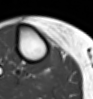
MRI of an extremity soft-tissue mass, one axial slice; slice 33 of 54 in the series (ordered by position); MR volume resampled by the dataset authors to the PET/CT grid (not the native acquisition matrix); 3.27 mm slice thickness; 93 × 99 image matrix, field of view 91 × 97 mm. Female patient. From the clinical record (not read from this slice): histological type: undifferentiated – high grade; grade: high; site of the primary tumour: right thigh.
Outlined on this slice (expert contour drawn on MRI and transferred to this co-registered scan by the dataset authors):
- gross tumour volume (mass): box from (x=47, y=45) to (x=64, y=69) px